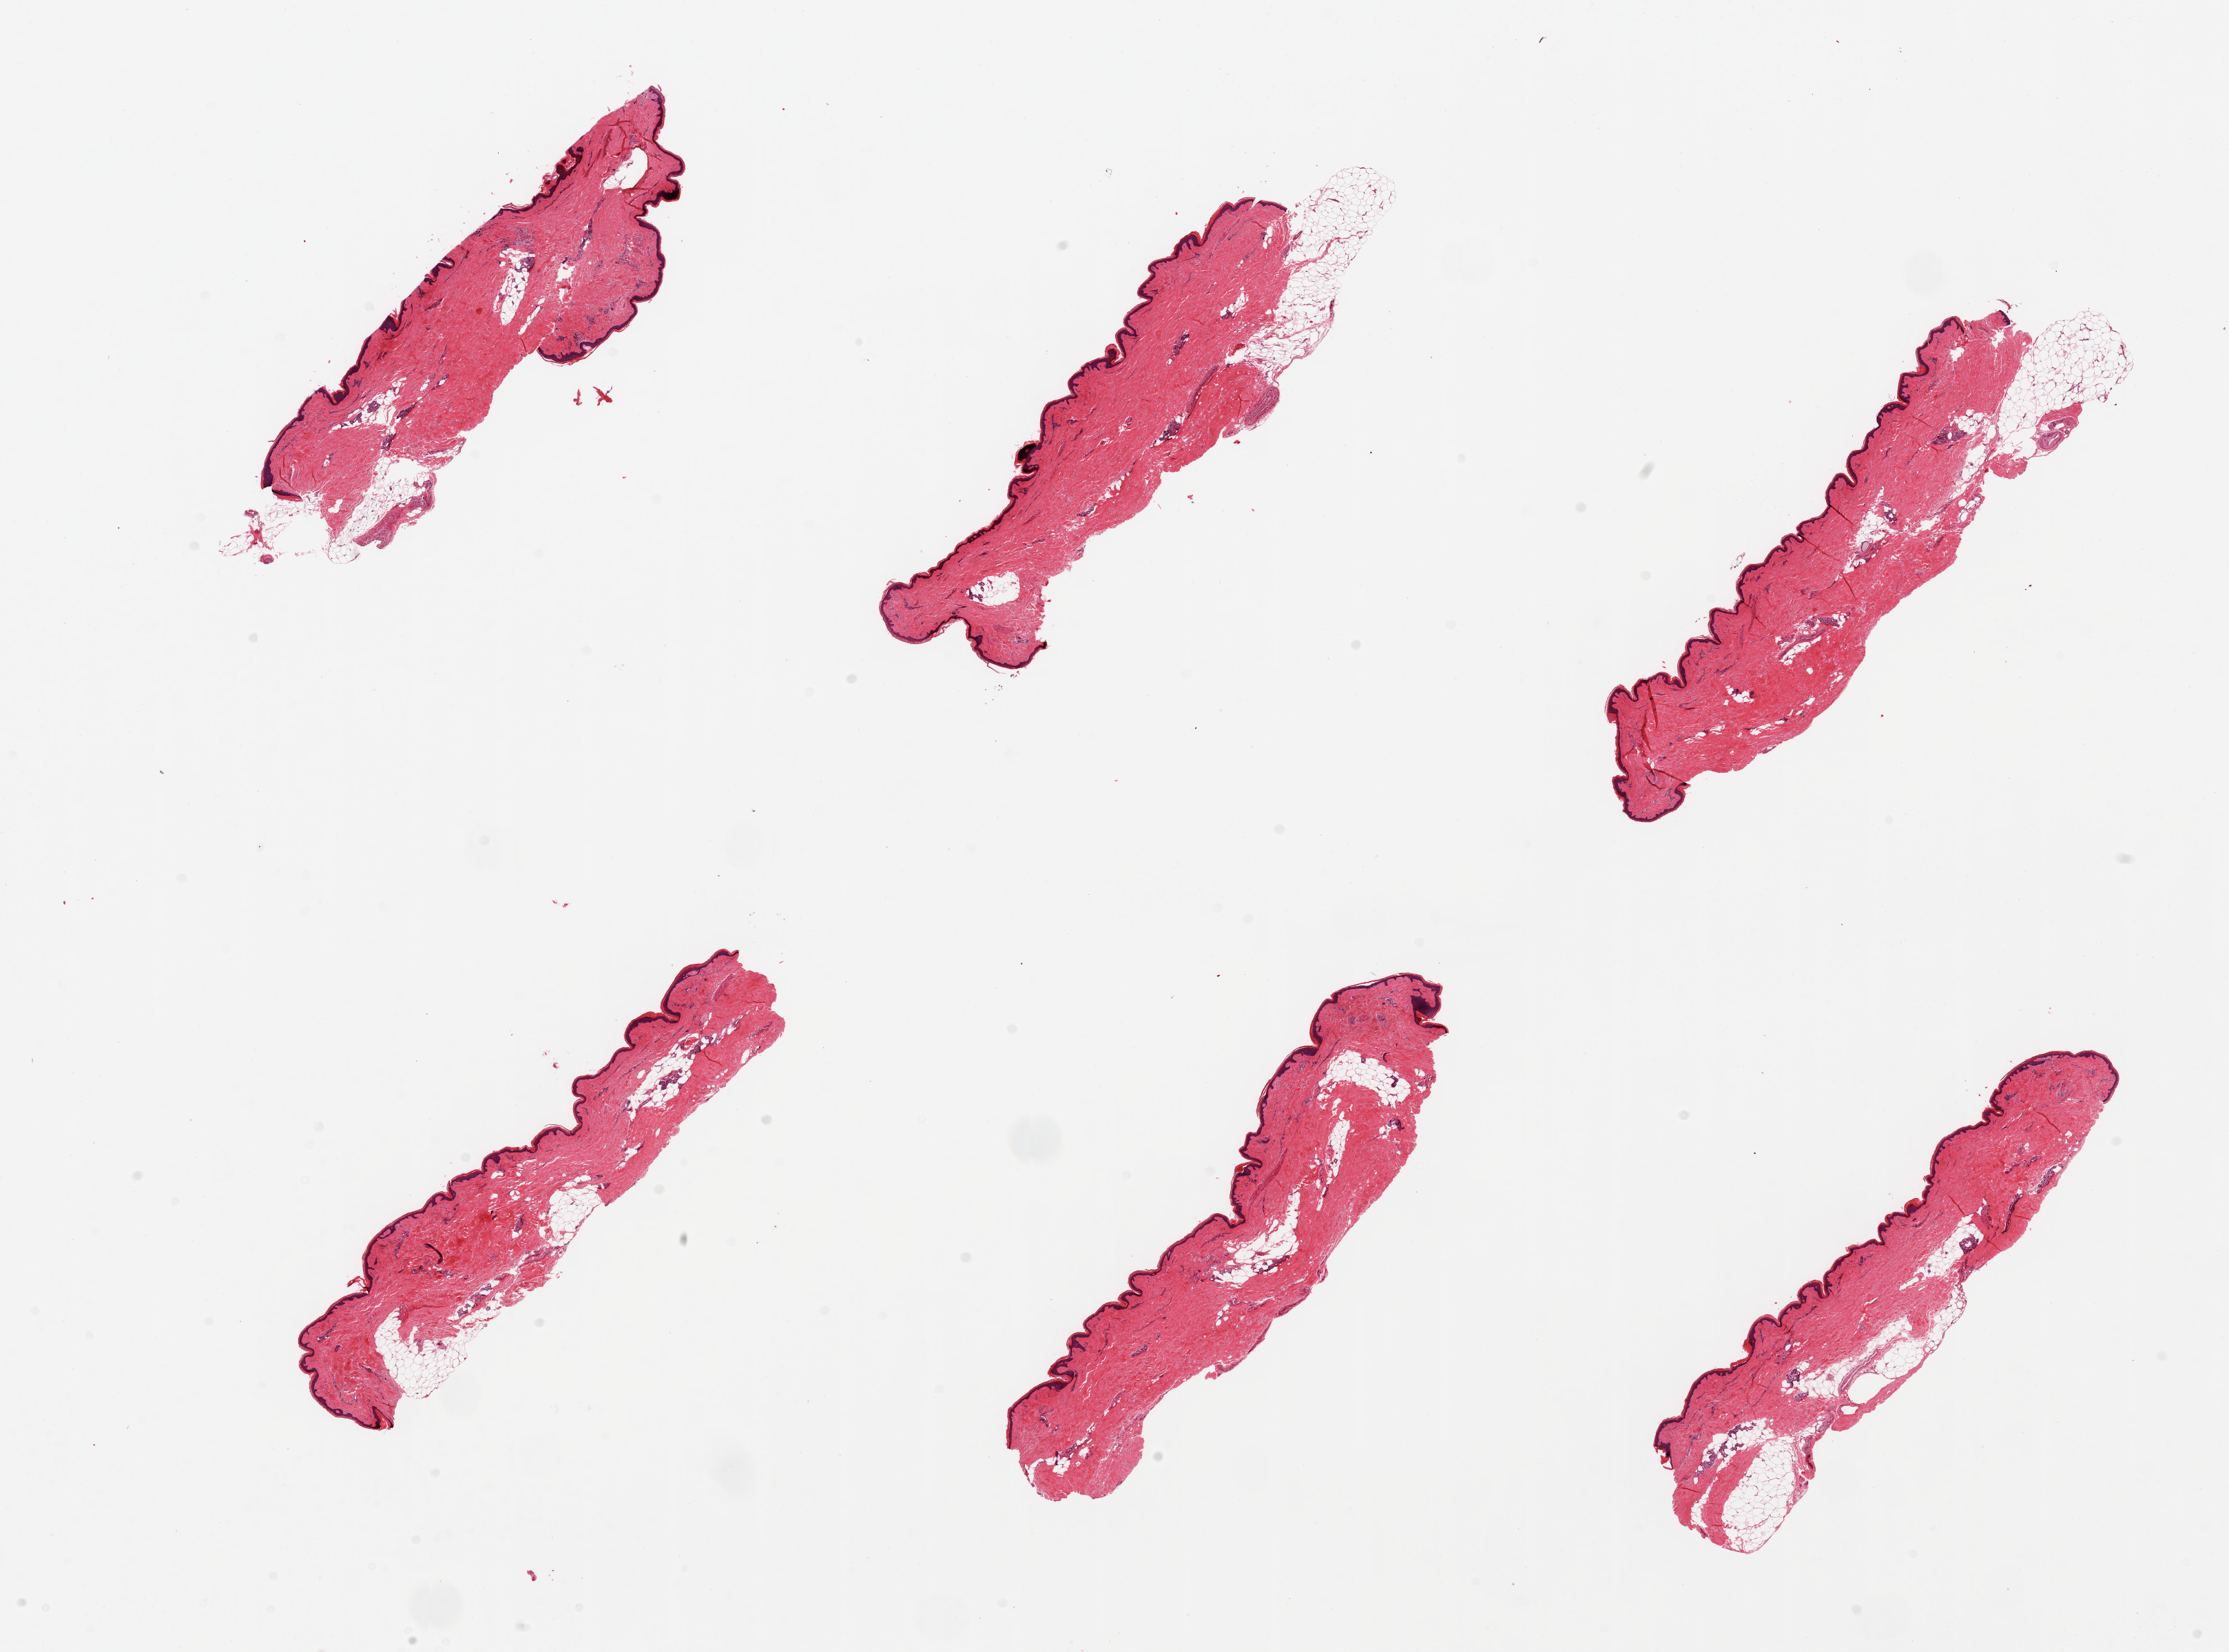
Haematoxylin and eosin whole-slide image, shown as a low-resolution overview of the whole scanned area (about 25.6 x 19.0 mm); PAXgene-fixed, paraffin-embedded tissue; section of skin of lower leg (target tissue); tissue donor sample. Male donor.
Pathologist's review note for this sample: 6 pieces, minimal dermal fat; squamous epithelium is ~30-40 microns.